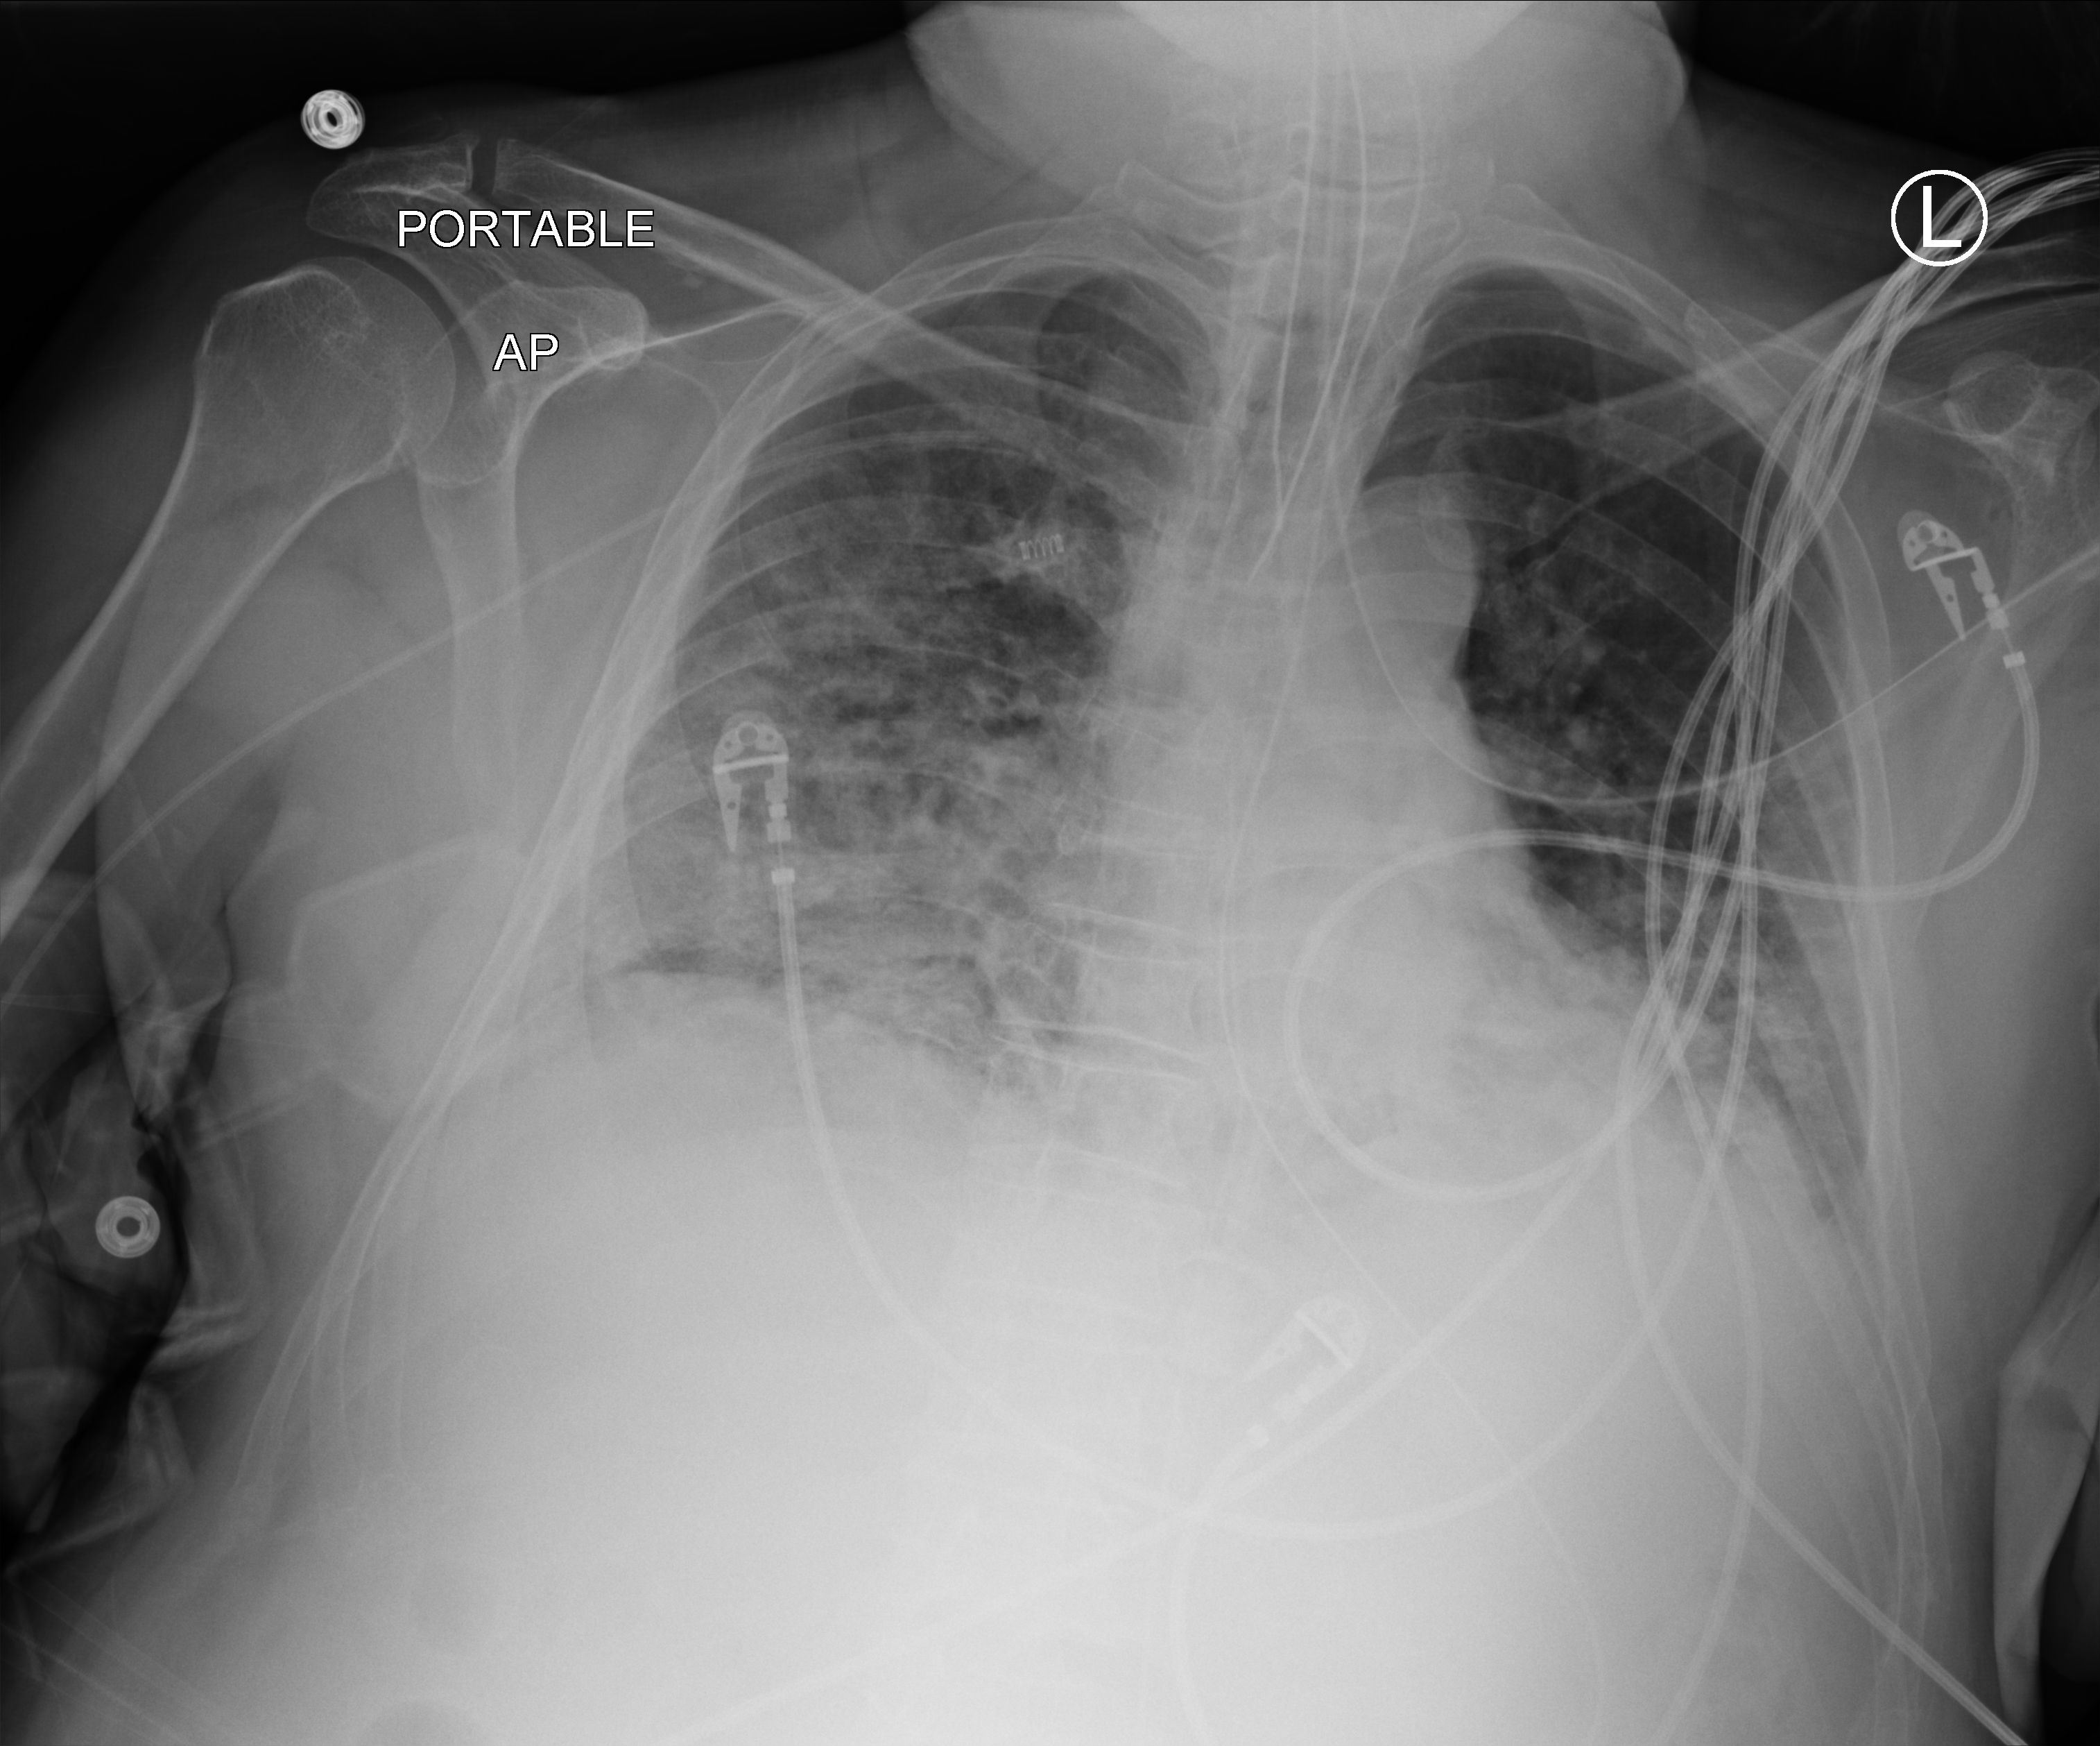
Chest X-ray (portable), anteroposterior (AP) projection. Male patient hospitalised with COVID-19, age 60–74 years.
Admission-level facts for this patient (not findings on this image; timing relative to this image not recorded):
- length of hospital stay: 19 days
- mechanically ventilated during this hospital stay: yes